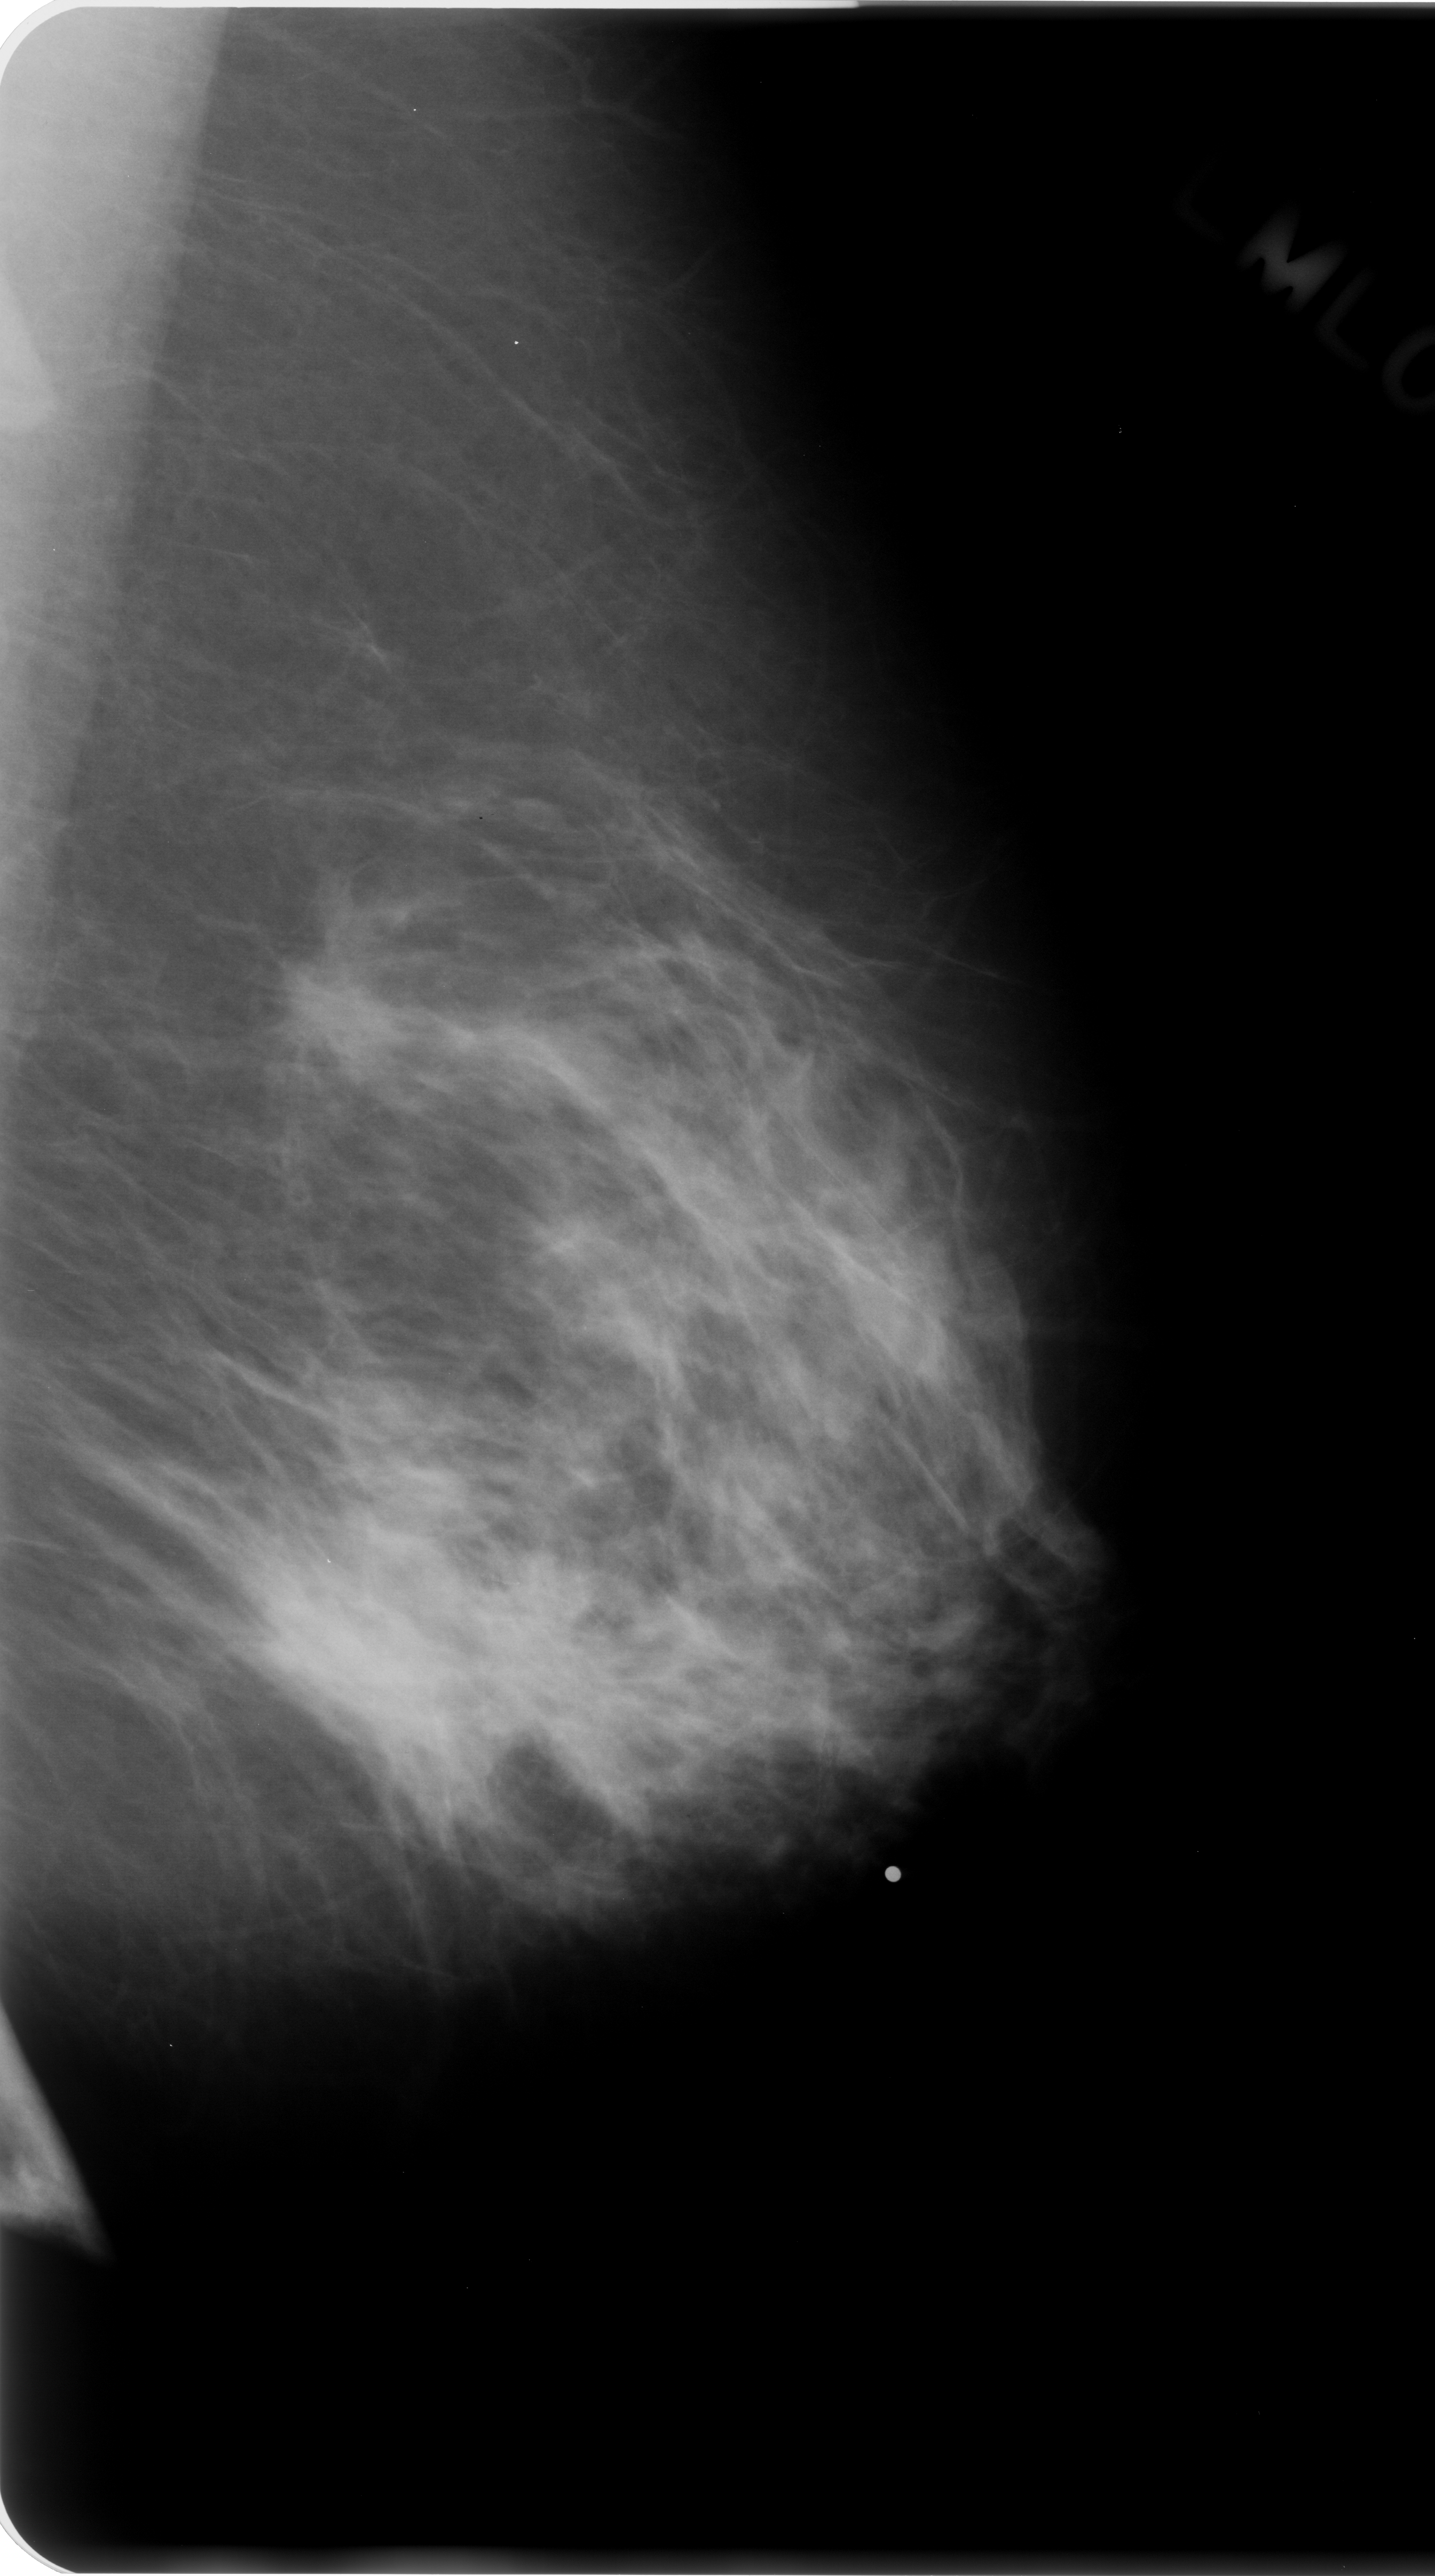
Scanned film-screen mammogram; left breast; mediolateral oblique (MLO) view; breast composition: scattered fibroglandular densities (BI-RADS density category 2 of 4); 1435 × 2576 image matrix.
Expert-marked regions of interest on this film, with their recorded descriptors:
- Finding 1 of 2: mass, shape irregular, margins spiculated; BI-RADS assessment category 5; pathology result (as recorded, not read from the image): malignant: bounding box (x1, y1, x2, y2) in pixels: (243, 921, 436, 1135)
- Finding 2 of 2: mass, shape irregular, margins ill defined; BI-RADS assessment category 5; subtlety rating 5 on a 1 (subtle) to 5 (obvious) scale; pathology (as recorded): malignant: (276, 1458, 602, 1761)